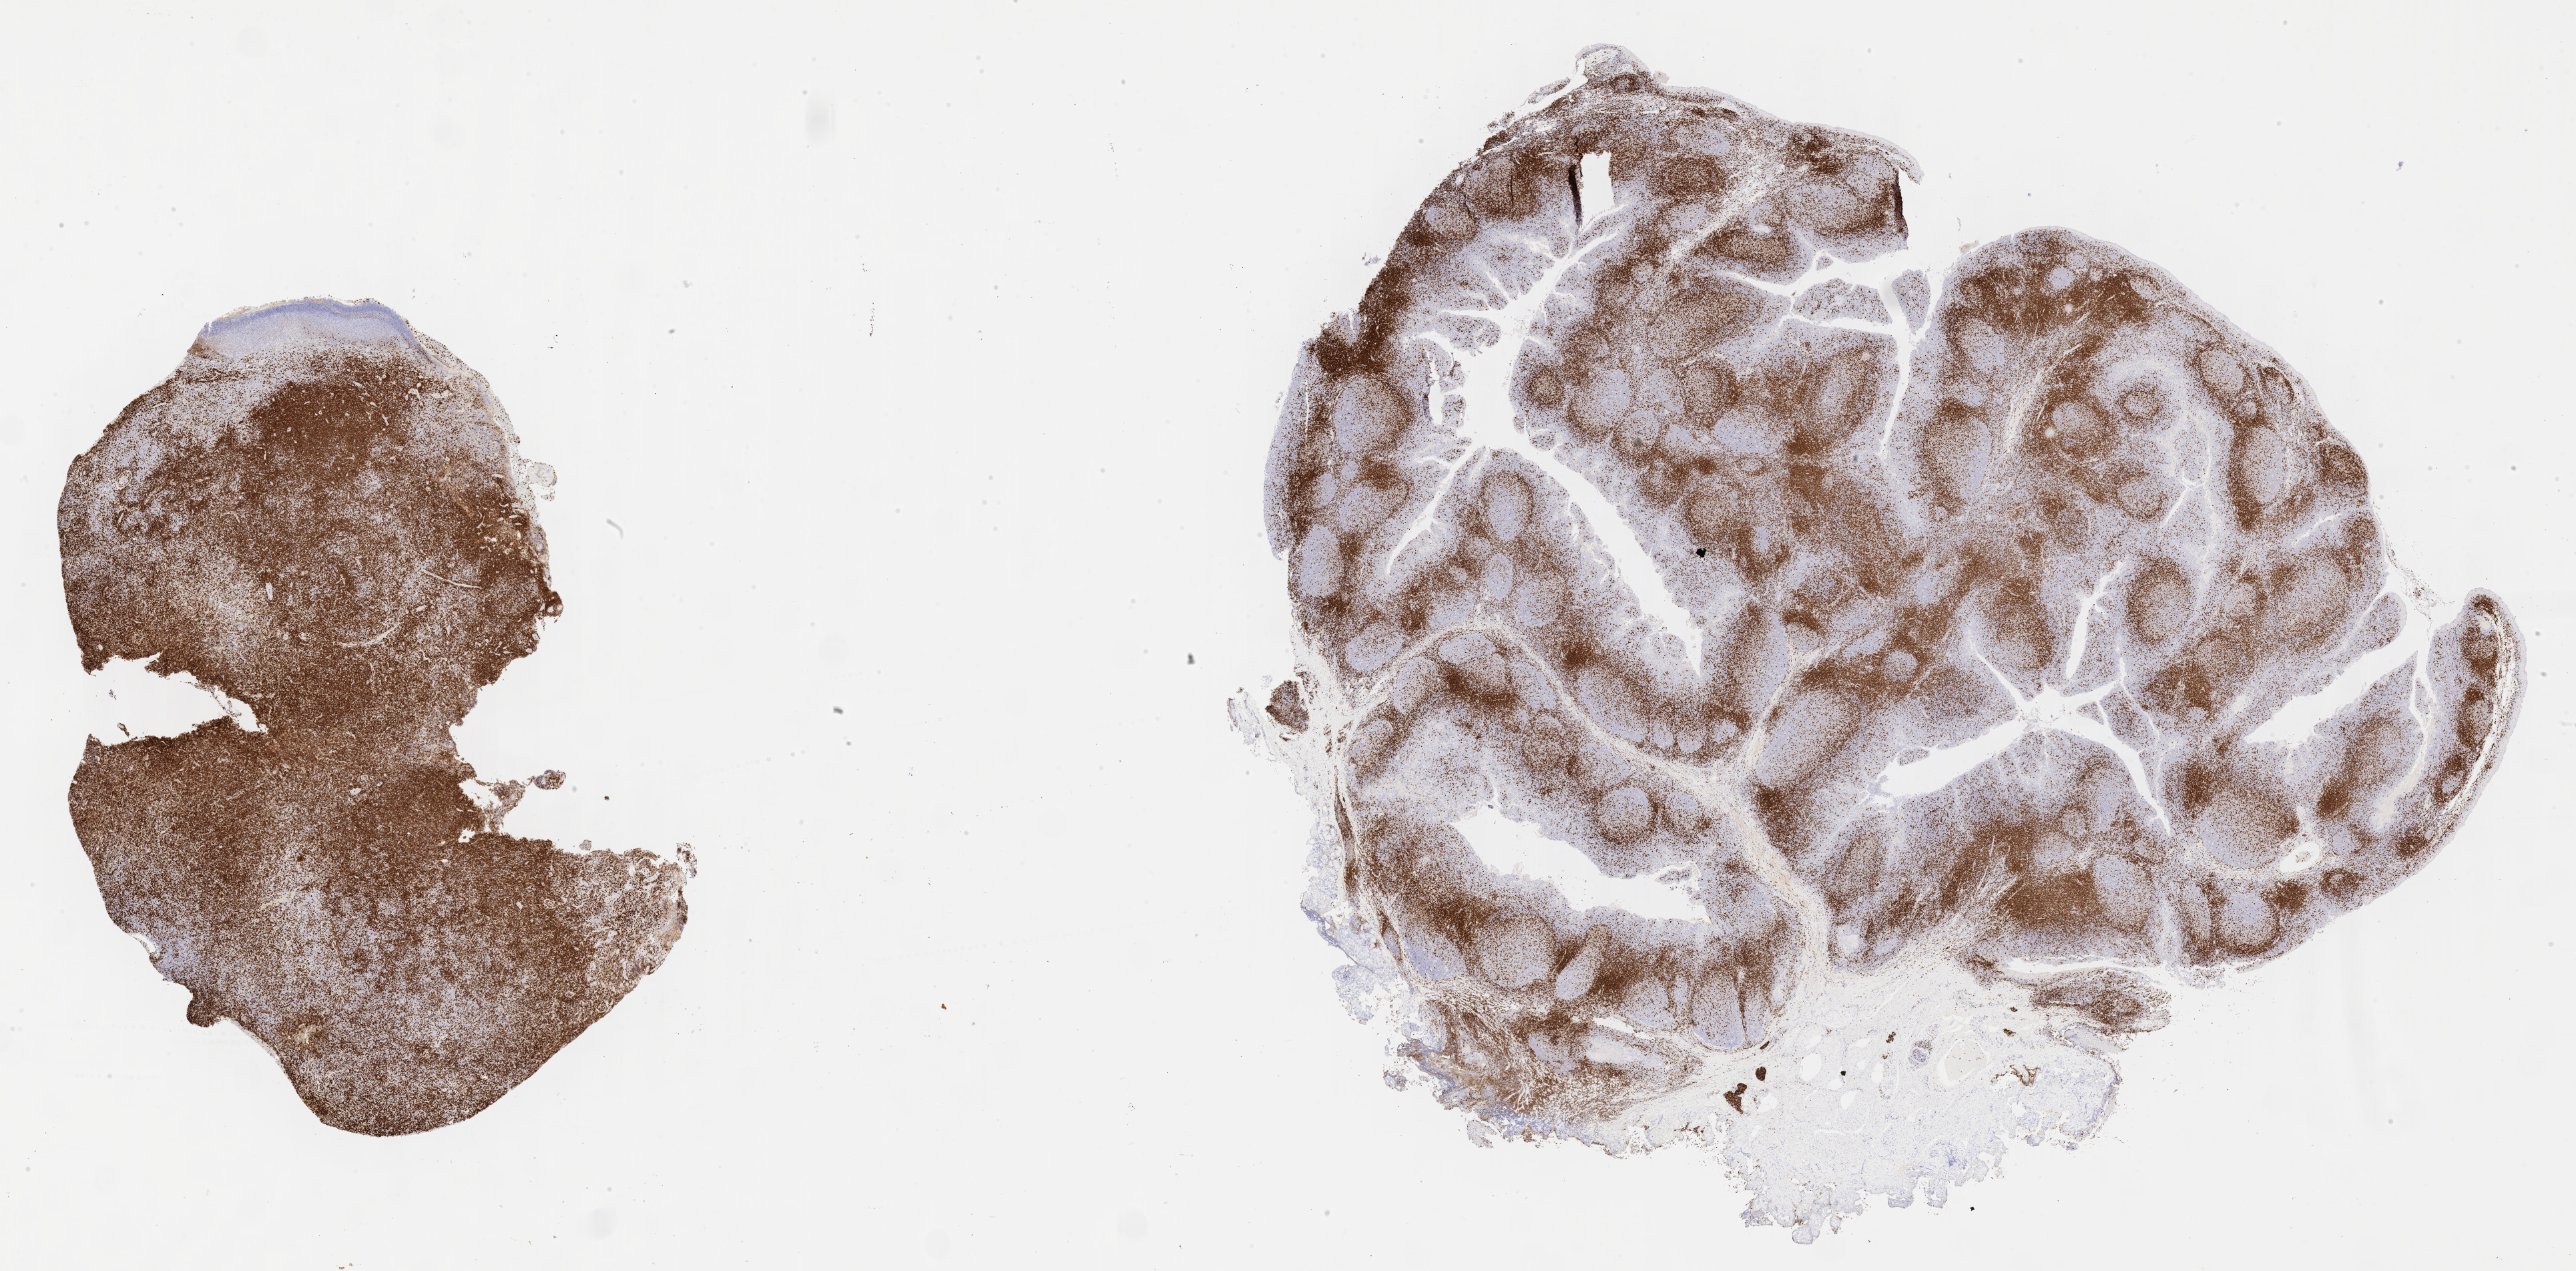
Whole-slide image, immunohistochemical stain for CD3 — a low-resolution overview of the entire scanned area, about 31.2 x 15.4 mm; tumor tissue. Male patient; age at initial diagnosis 7 years.
Histologic diagnosis: Diffuse large B-cell lymphoma, NOS.